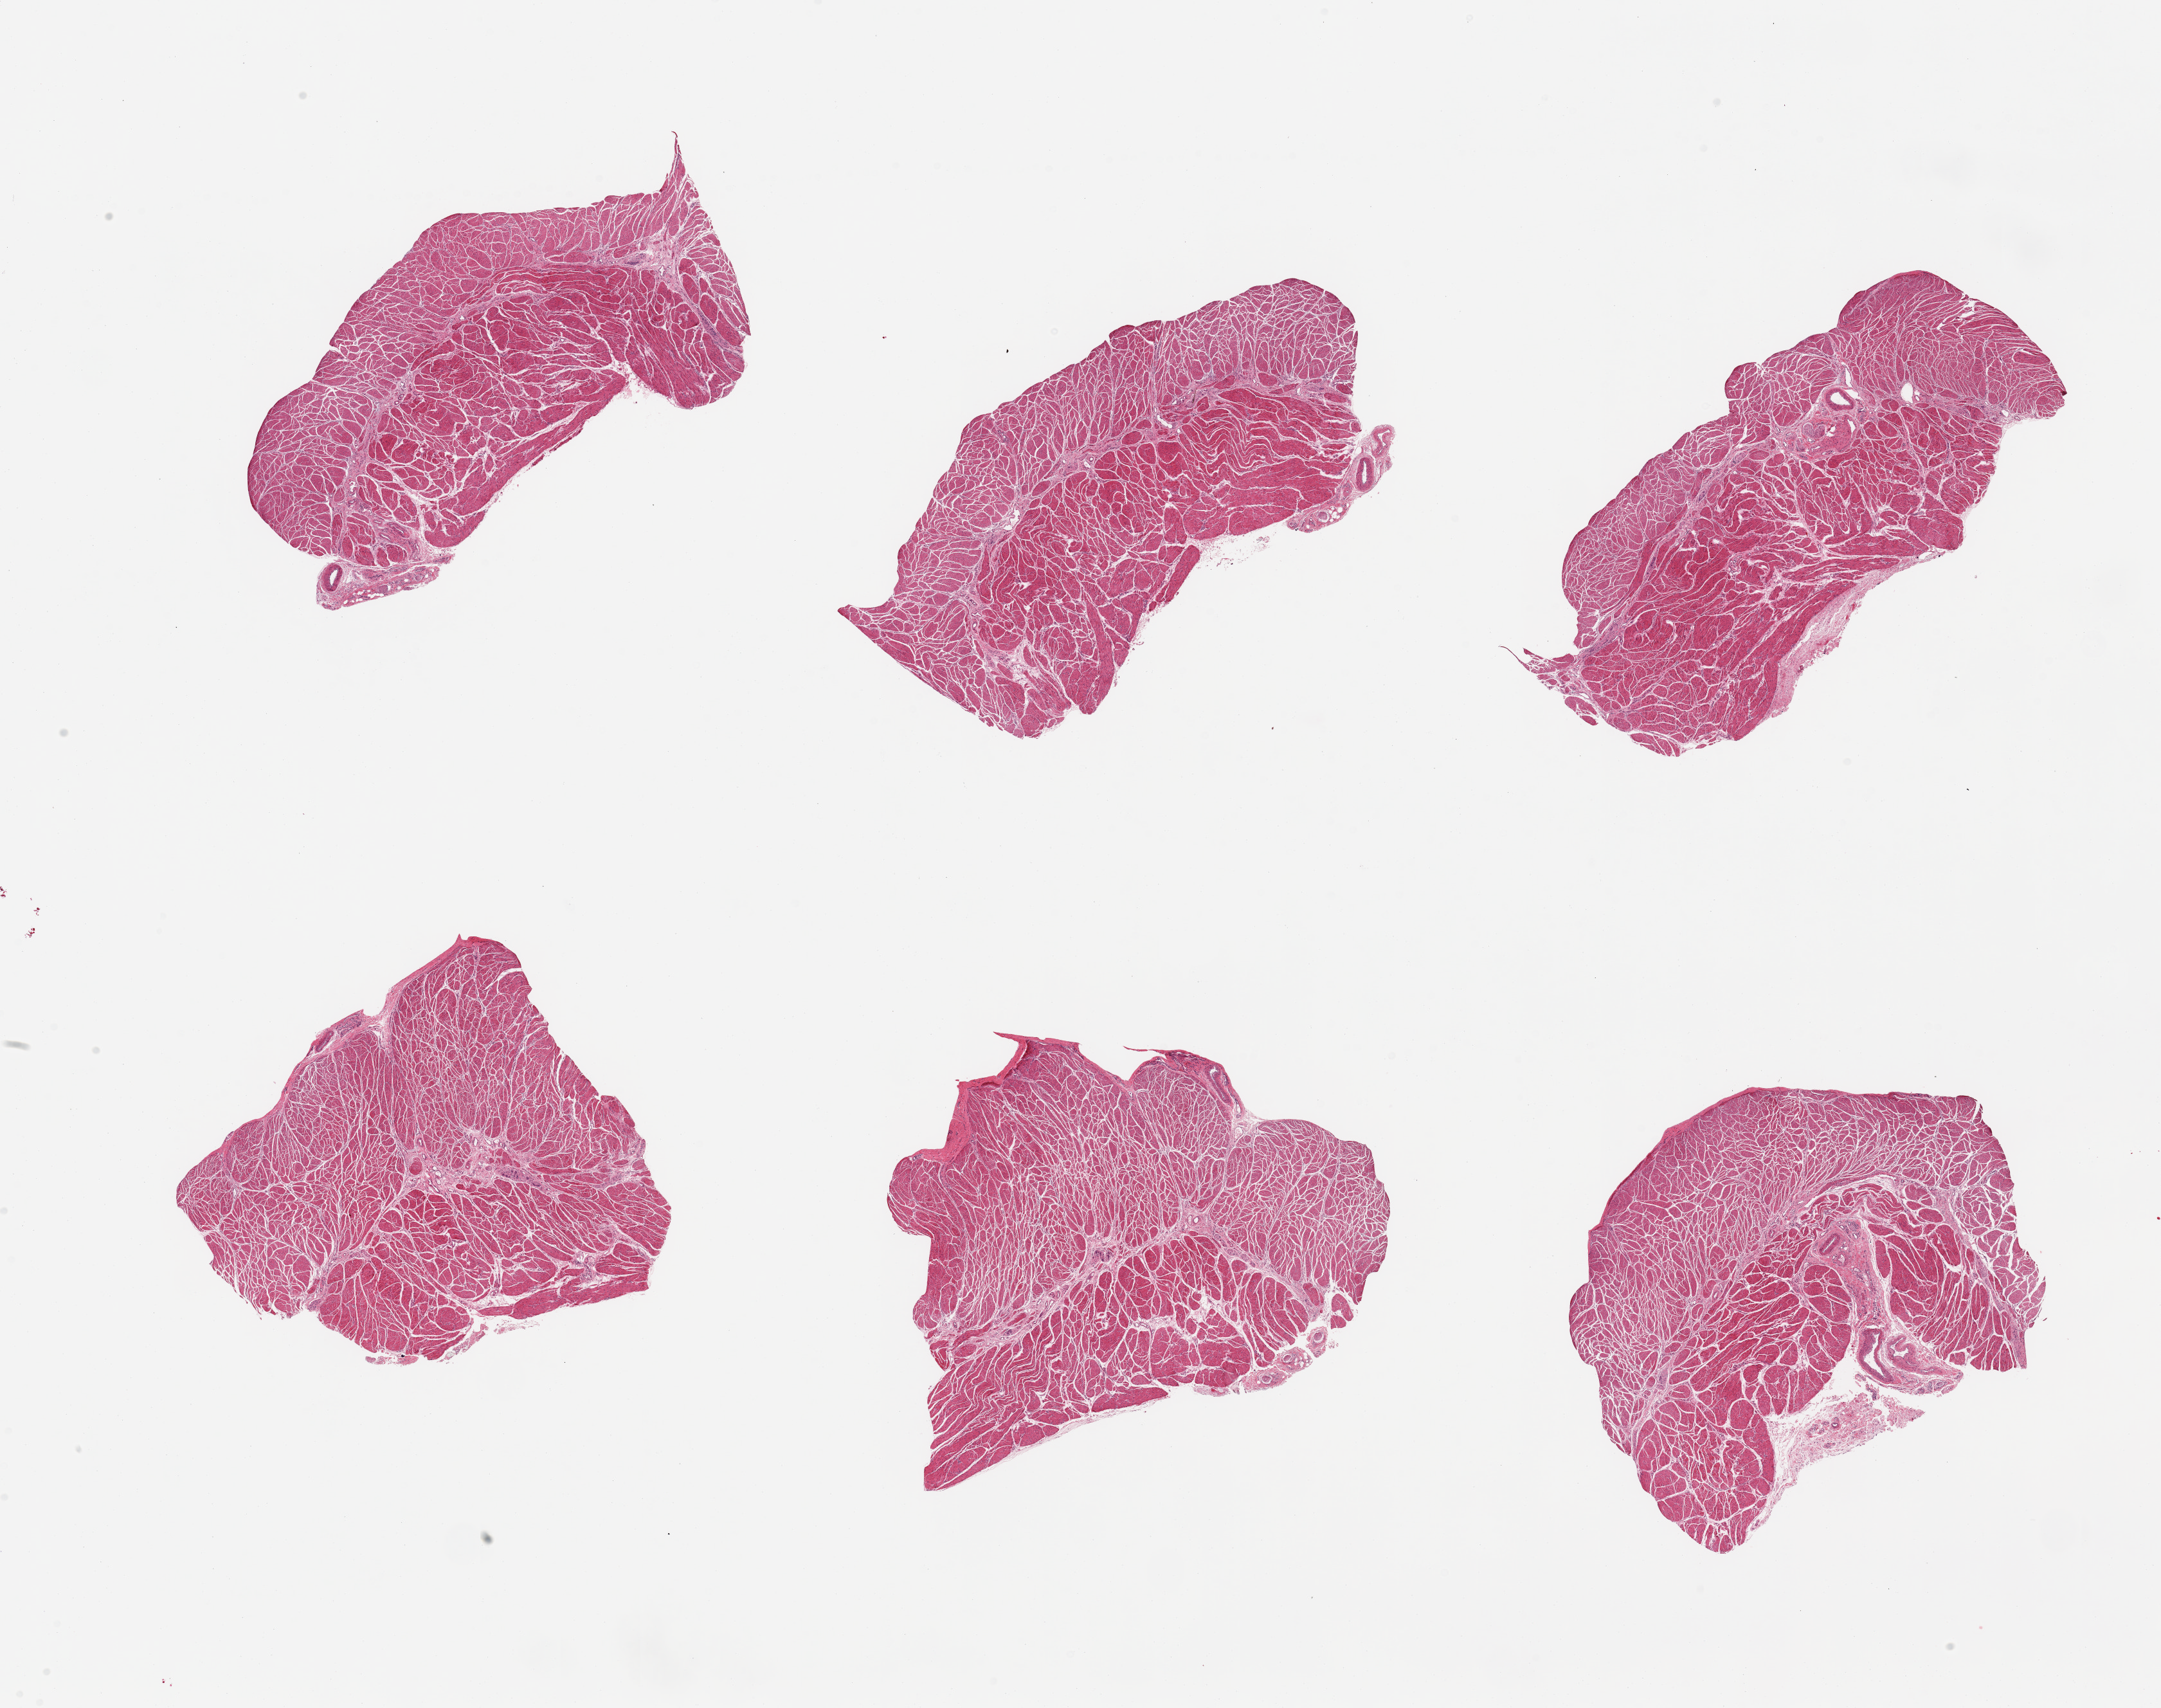
Whole-slide image, hematoxylin and eosin (H&E) stain, low-resolution overview of the scanned area, about 26.6 x 21.0 mm. PAXgene-fixed paraffin-embedded (PFPE) section. Section of esophageal muscle (target tissue). Donor tissue sample.
- review note (as recorded): 6 pieces; well dissected